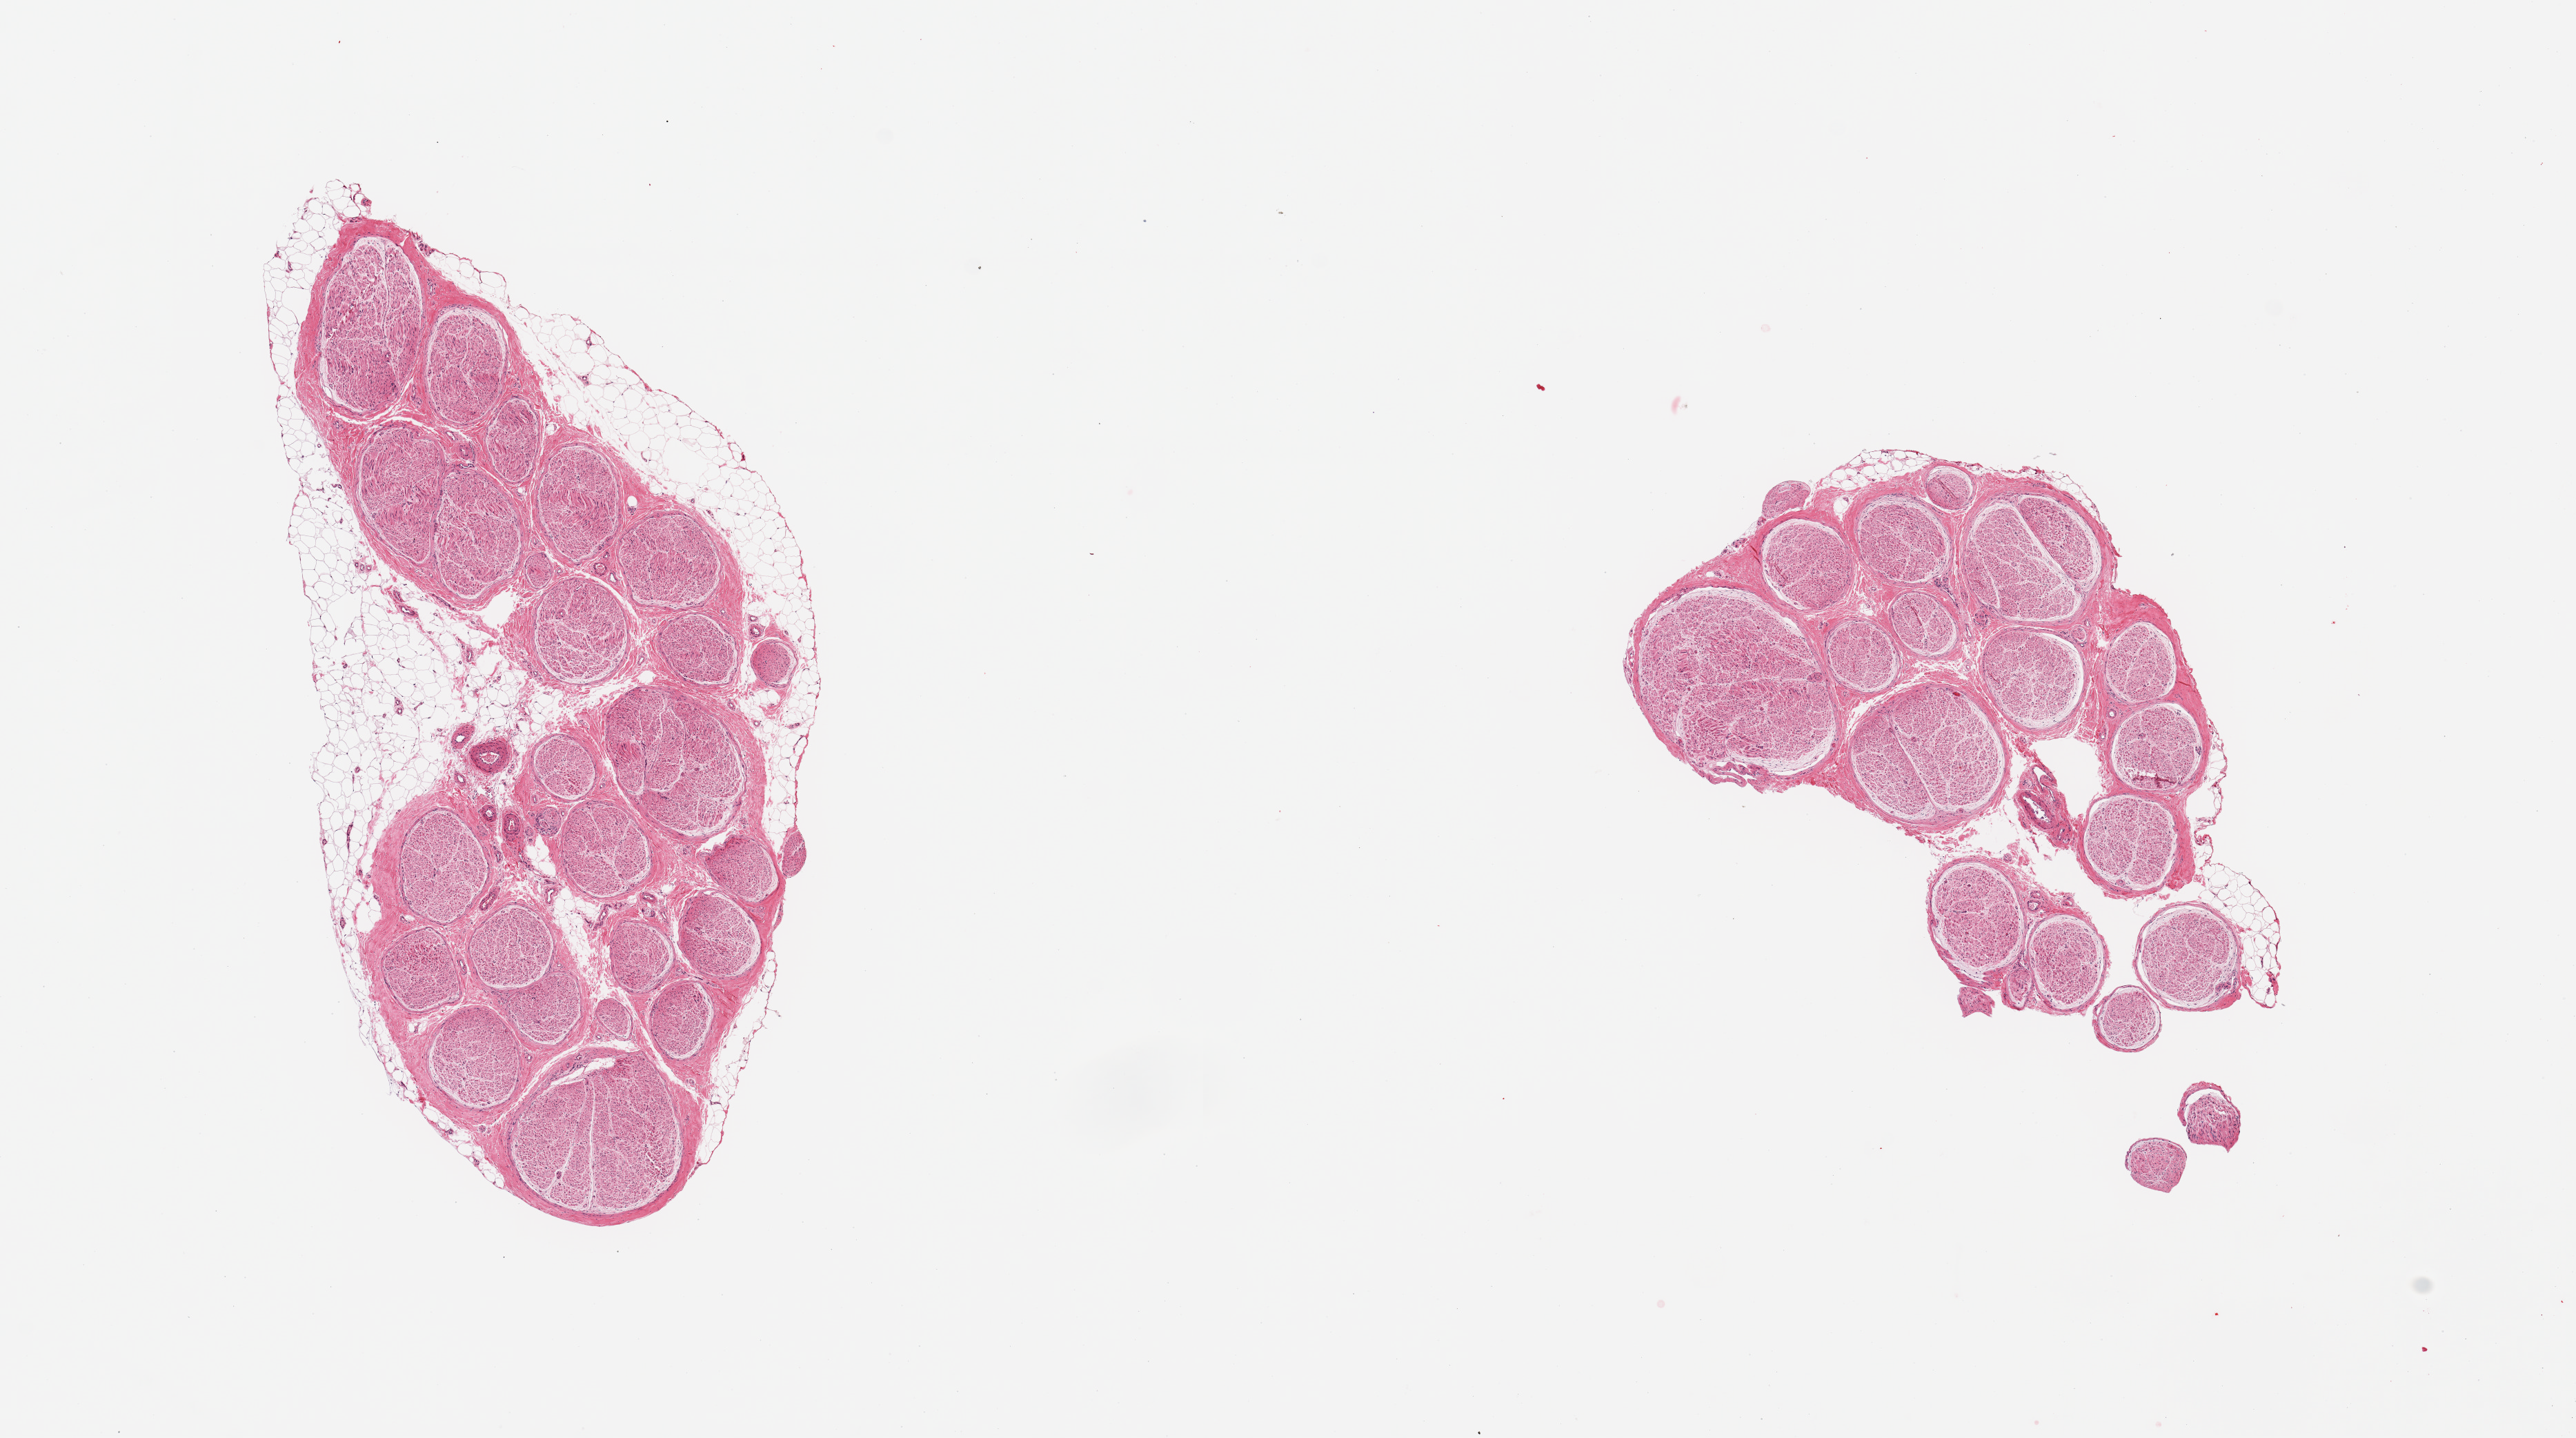
Digitized haematoxylin and eosin-stained section, brightfield, shown as a low-resolution overview of the whole scanned area (about 14.8 x 8.2 mm, from a 20x scan), PAXgene-fixed, paraffin-embedded tissue, target tissue: tibial nerve, donor tissue sample. Donor sex: female.
Pathologist's review note for this sample: 2 pieces: 30% external fat on 1.